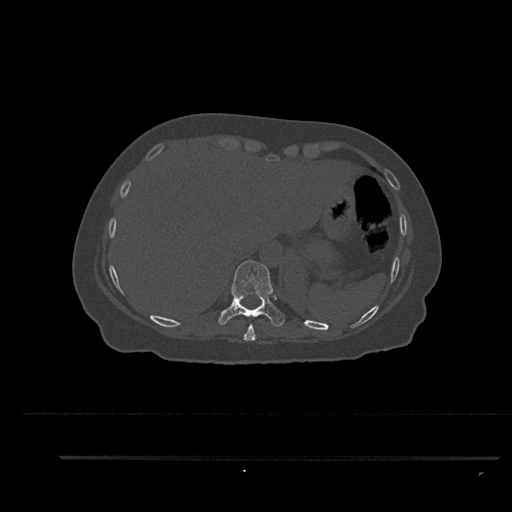
CT including the spine, one axial slice. Position 371 of 797 along the scan axis. 120 kVp. Bone window (W 1800 / L 400 HU). 0.5 mm slice thickness. 512 × 512 image matrix, field of view 408 × 408 mm. Patient: female, 44 years. From the clinical record (not read from this slice): primary cancer: renal; vertebrae with lytic lesions (as recorded): L1.
Annotated regions visible in this slice (semi-automatically segmented with operator editing):
- T10 vertebra: bounding box (x1, y1, x2, y2) in pixels: (218, 260, 285, 328)
- T9 vertebra: (243, 325, 257, 341)